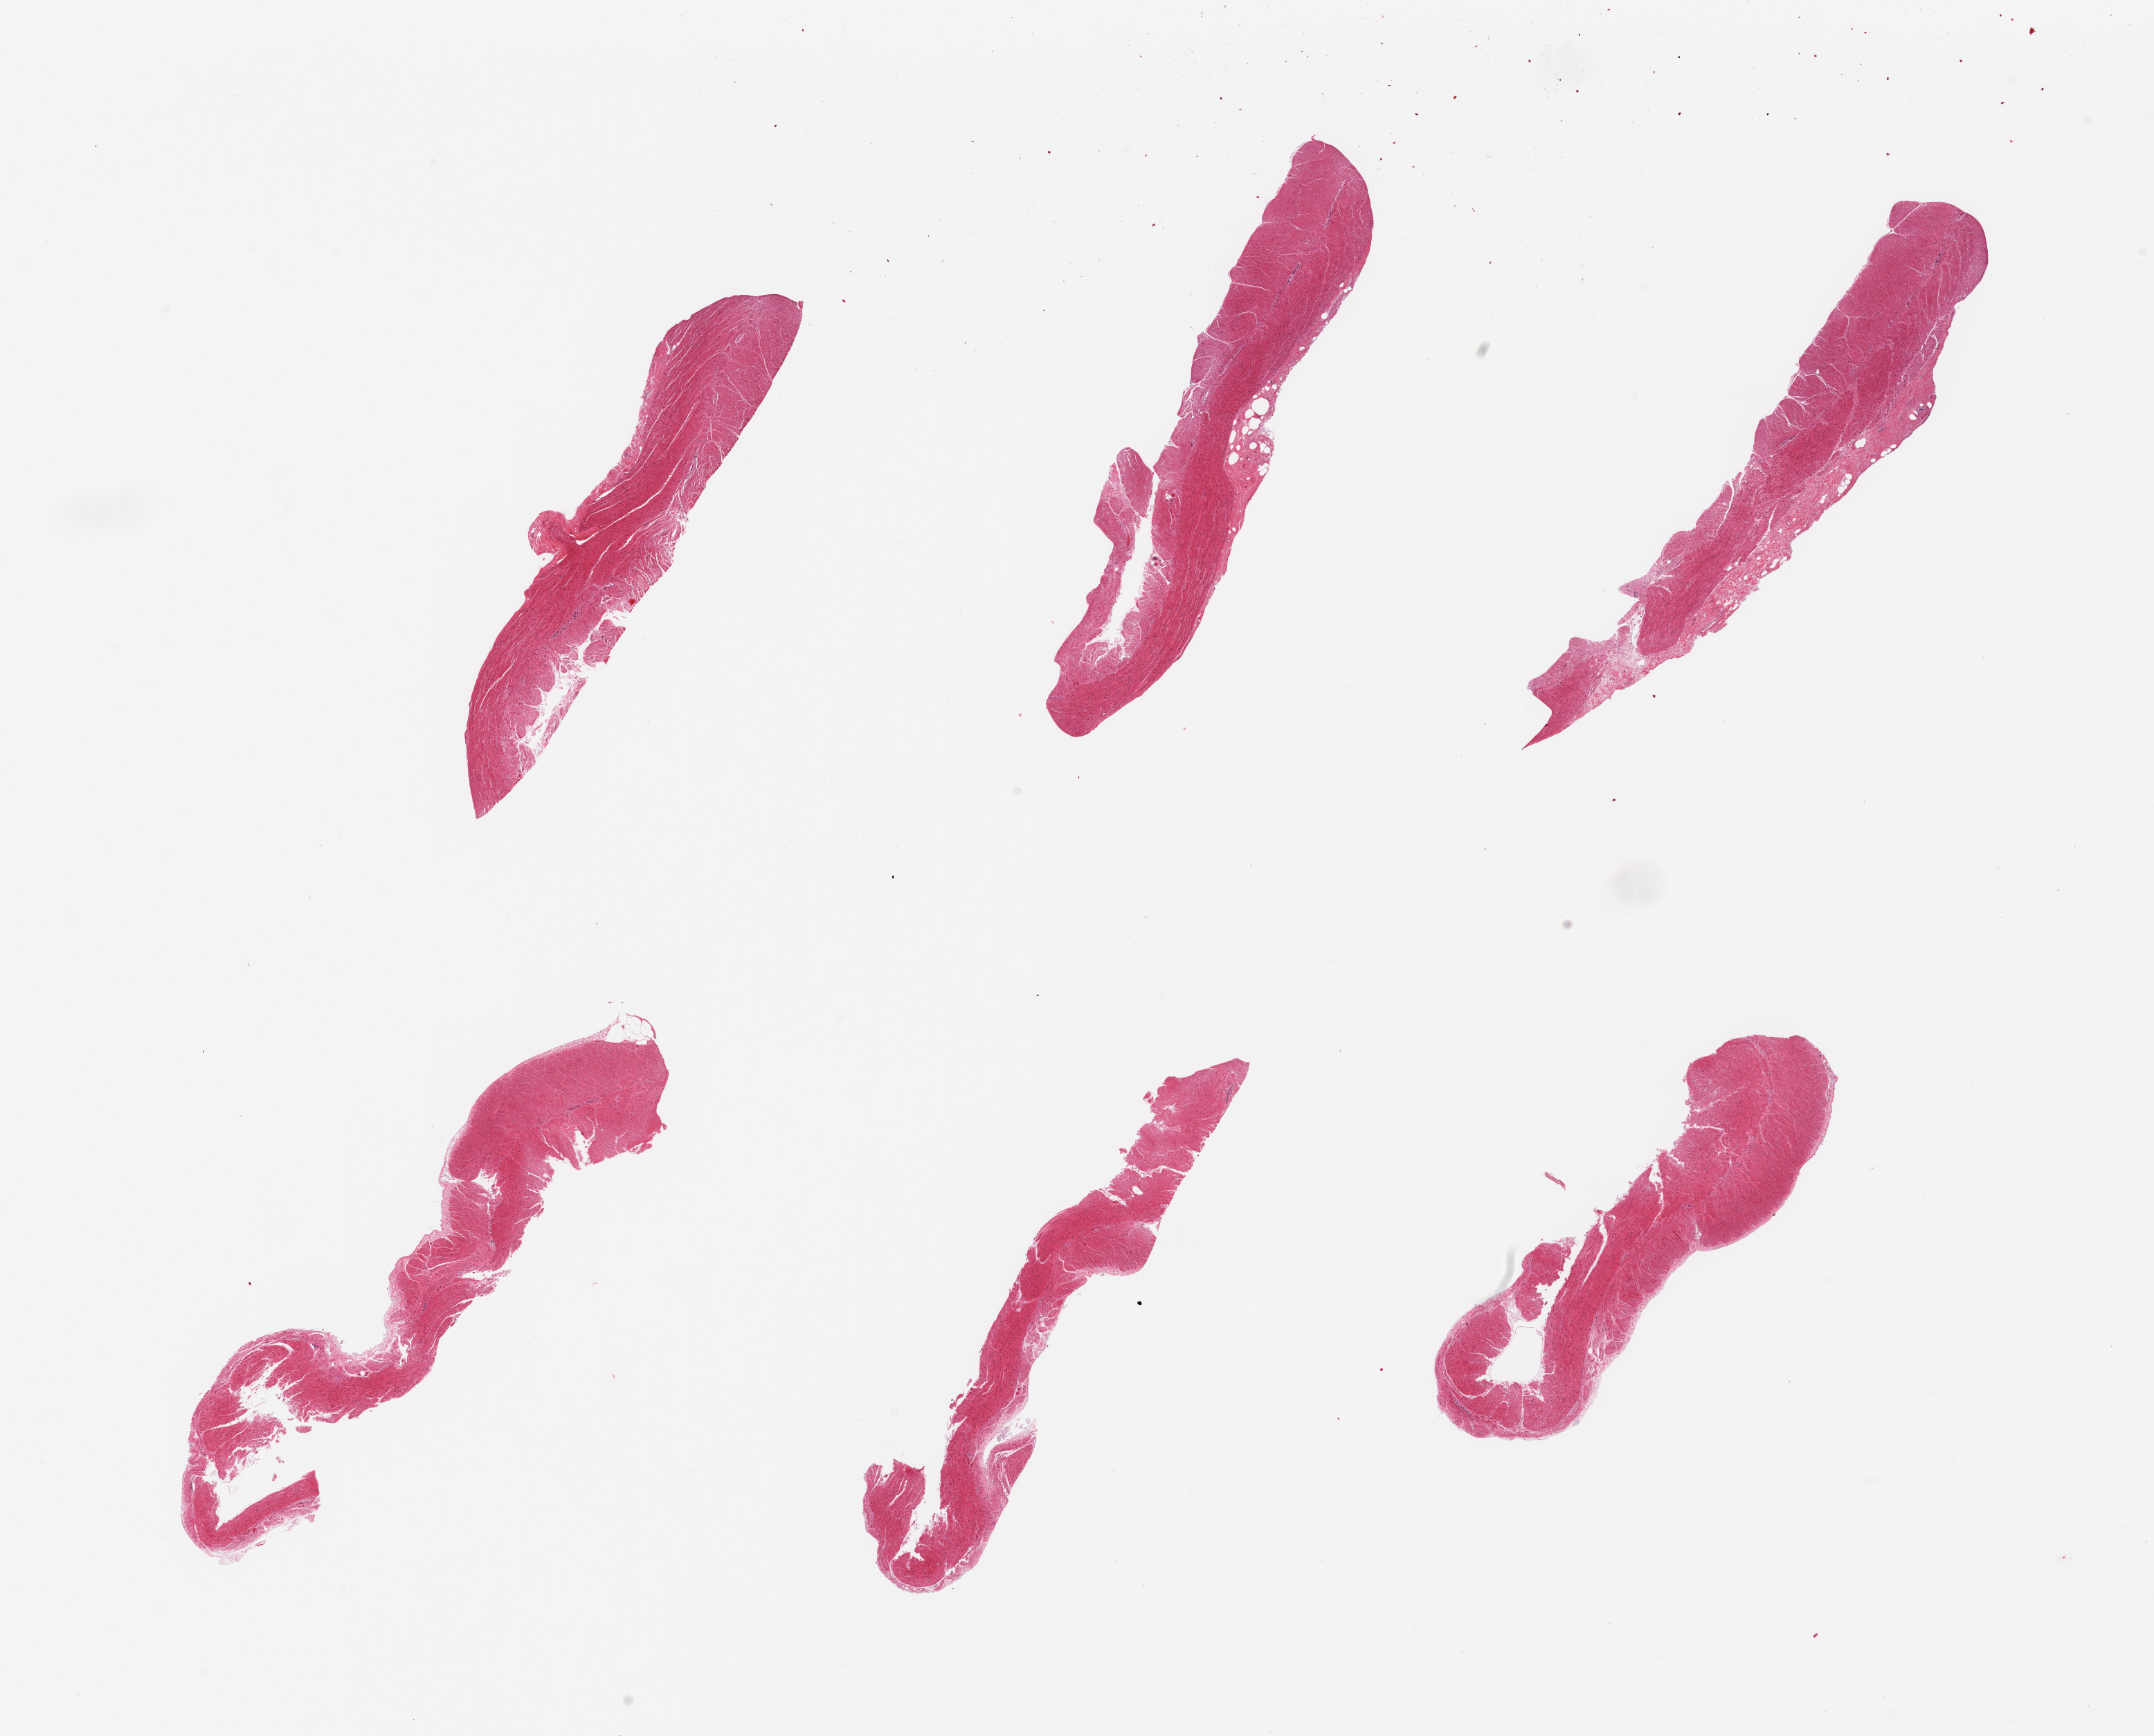
Hematoxylin and eosin (H&E) whole-slide image, shown as a low-resolution overview of the whole scanned area (about 24.6 x 19.8 mm), PAXgene-fixed paraffin-embedded (PFPE) section, target tissue: sigmoid colon, donor tissue sample. Donor: male.
Reviewer comment on this tissue sample: 6 pieces; target muscularis.